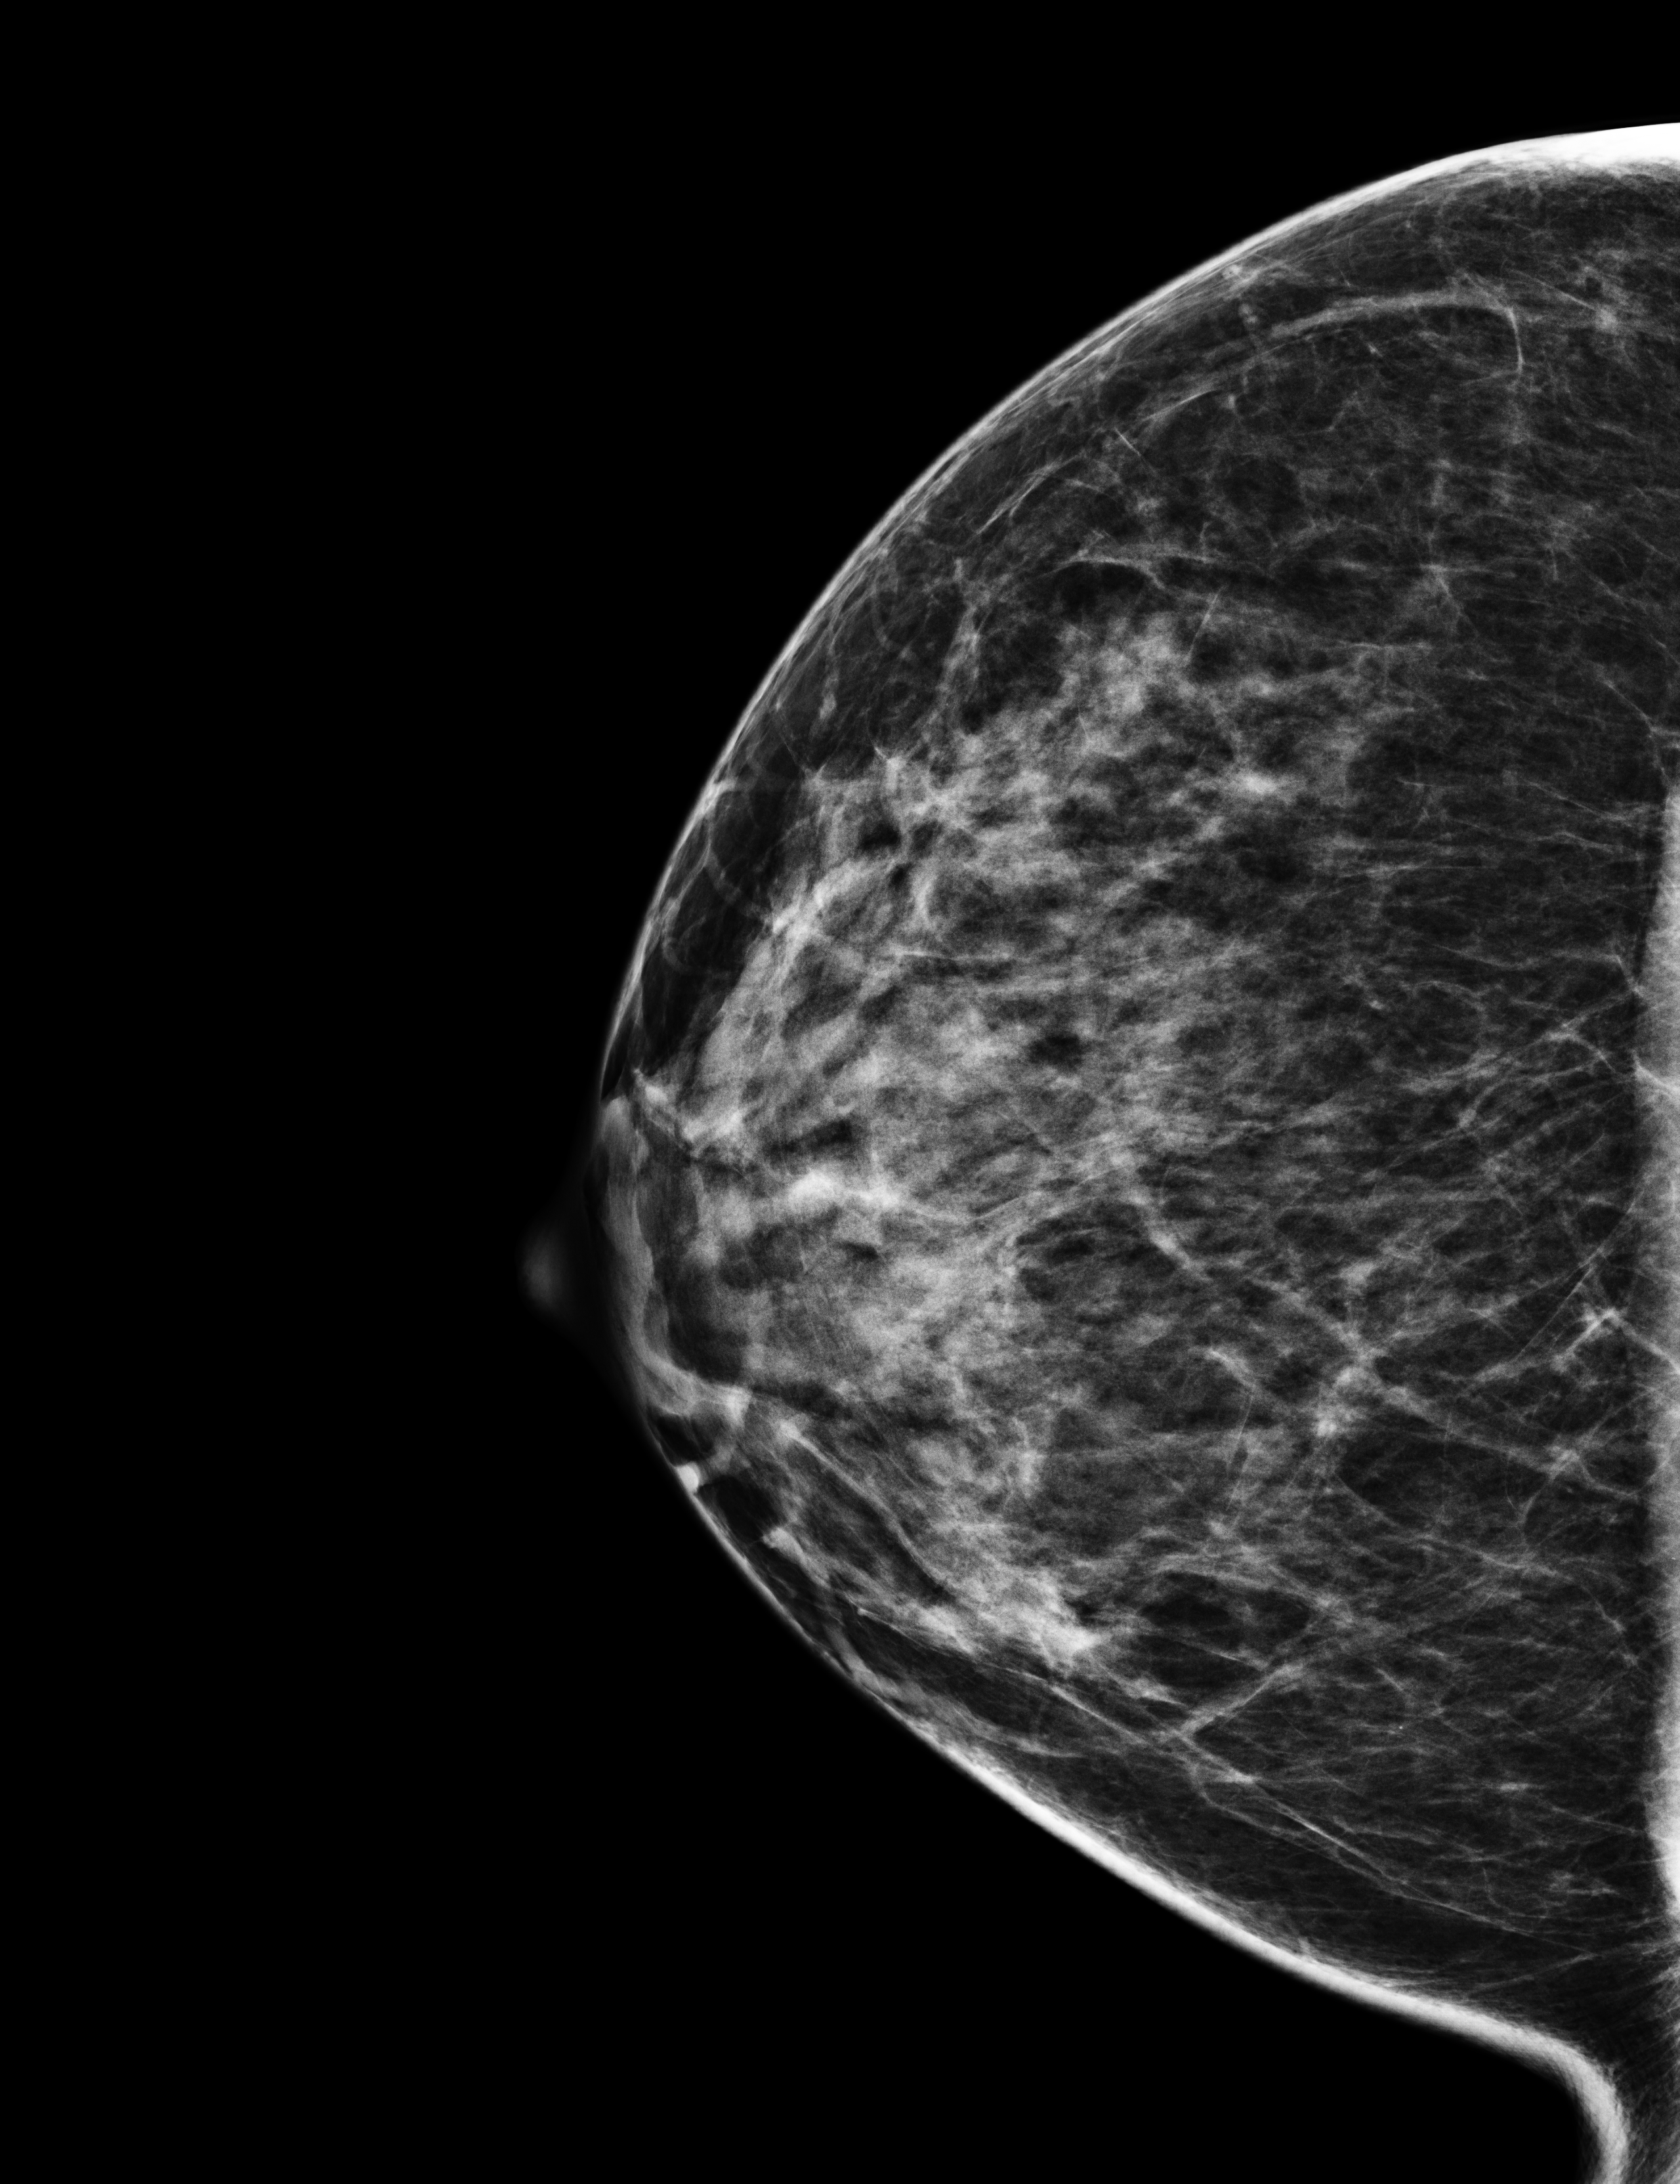
Digital mammogram (FFDM), right breast, craniocaudal (CC) view, screening examination. Patient aged 43 years (female).
Breast density at the screening exam (both breasts): heterogeneously dense (BI-RADS density category c). Final BI-RADS category for the screening round (tomosynthesis exam, both breasts): category 1. Recall: no recall after this screen.